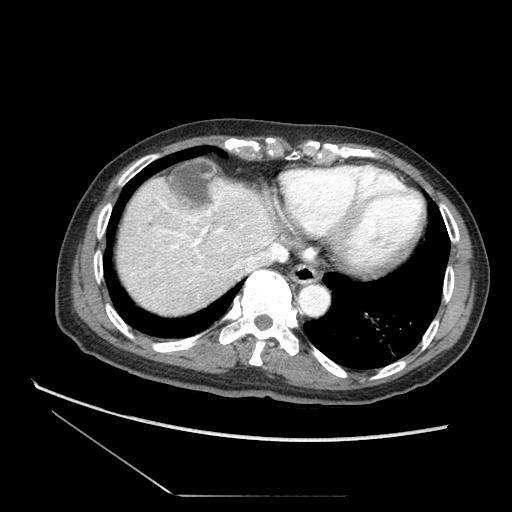
Contrast-enhanced abdominal CT (liver protocol), one axial slice; position 66 of 73 along the scan axis; soft-tissue window (W 400 / L 40 HU); 2.5 mm slice thickness; 512 × 512 image matrix, field of view 360 × 360 mm. Case-level facts recorded for this patient, not image findings: diagnosis: hepatocellular carcinoma (patient treated with transarterial chemoembolisation; whether this scan precedes or follows treatment is not stated here); TNM stage (as recorded): Stage-II; Child-Pugh class: A; tumour differentiation: moderately differentiated.
Annotated regions visible in this slice (semi-automatic segmentation, software-assisted and operator-edited):
- abdominal aorta: bounding box <301,285,330,315> (left, top, right, bottom; pixels)
- liver parenchyma outside the tumour (the mass and vessels are separate outlines, so this box may not span the whole liver): <112,178,284,321>
- mass: <120,264,152,298>
- liver vessels: <200,235,209,244>